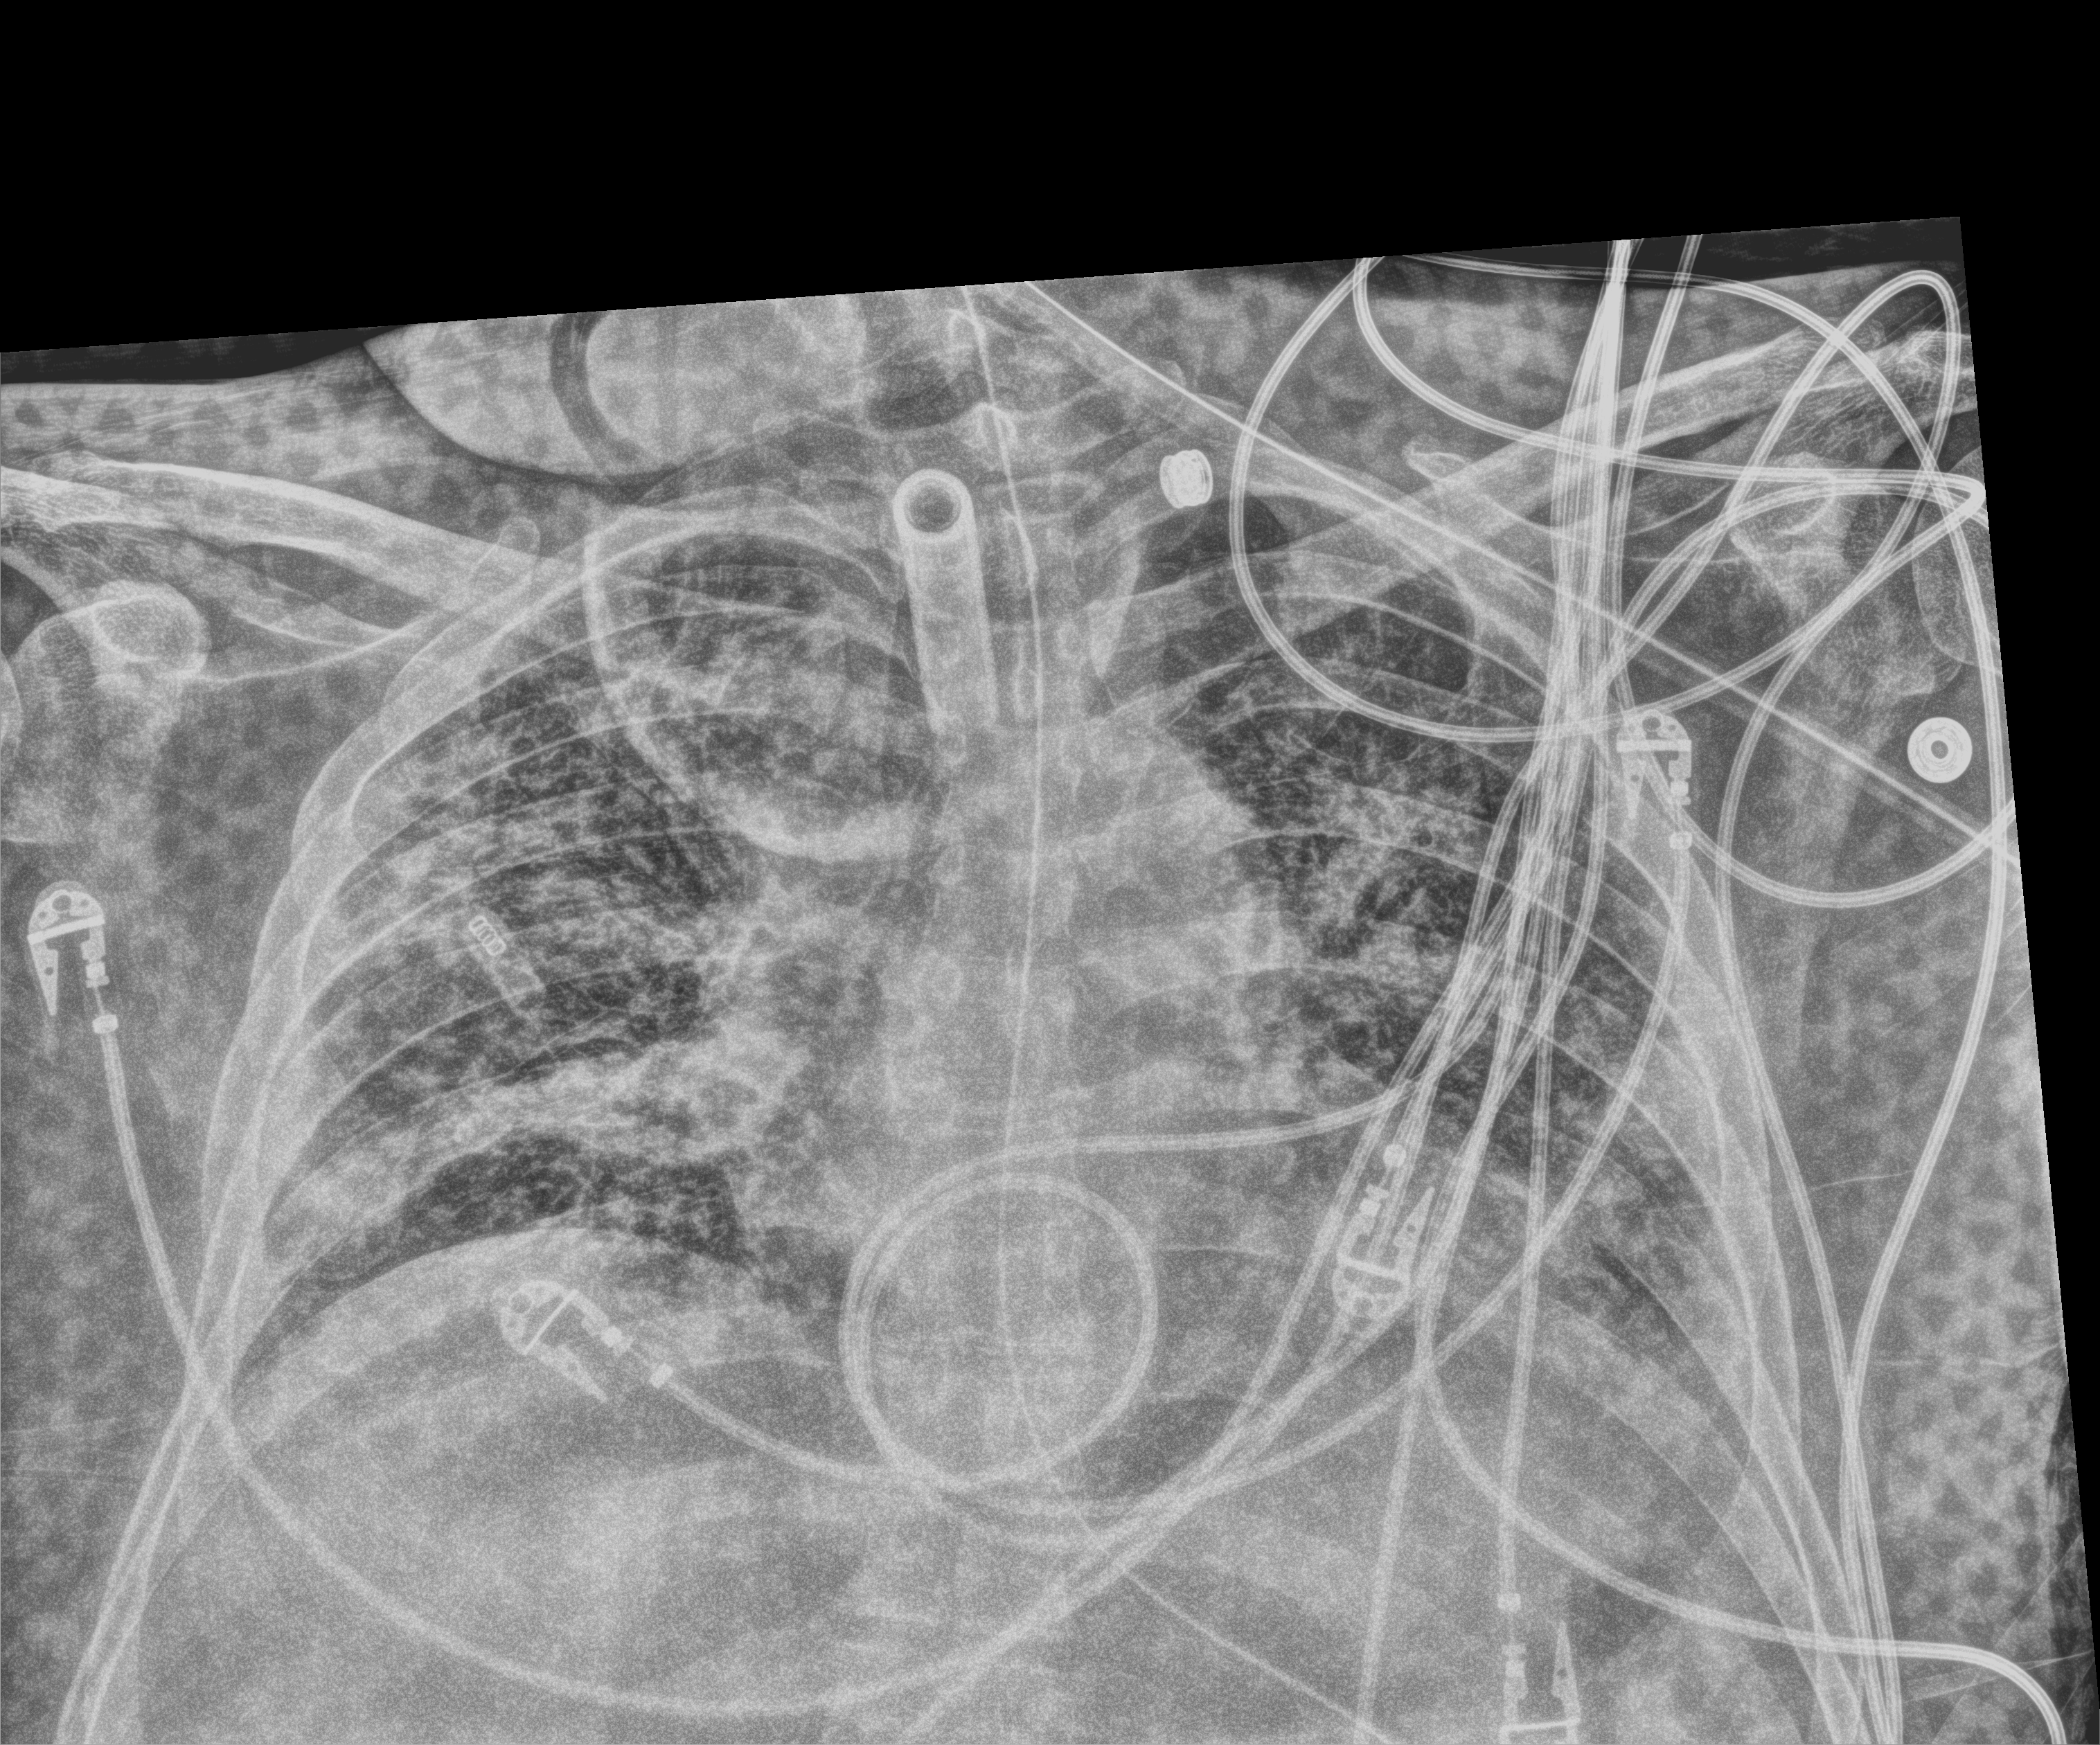
Bedside chest radiograph (digital radiography). Patient hospitalised with COVID-19; male, aged 18–59 years.
From the hospital-stay record, not from the radiograph (when in the stay this image was taken is not recorded):
- length of hospital stay: 63 days
- diabetes (admission record): yes
- other chronic lung disease (admission record): no